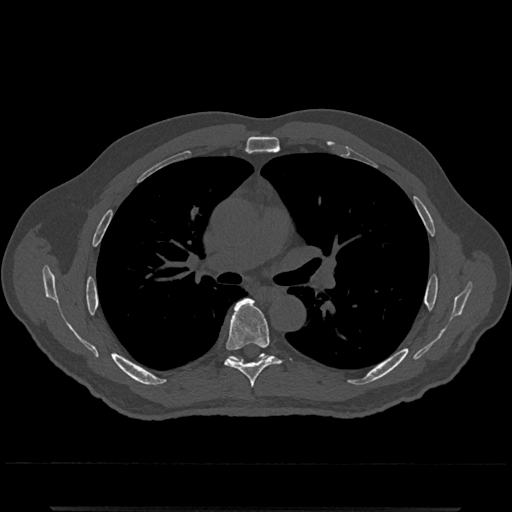
CT including the spine, one axial slice; reconstruction kernel Br40s/3; 120 kVp; bone window (W 1800 / L 400 HU); 0.5 mm slice thickness; 512 × 512 image matrix, field of view 393 × 393 mm. Male patient, age 67 years. Case-level facts recorded for this patient, not image findings: primary cancer: prostate.
Structures marked on this image (semi-automatic segmentation, software-assisted and operator-edited):
- T6 vertebra: bounding box <224,299,280,388> (left, top, right, bottom; pixels)
- T7 vertebra: <229,354,268,362>